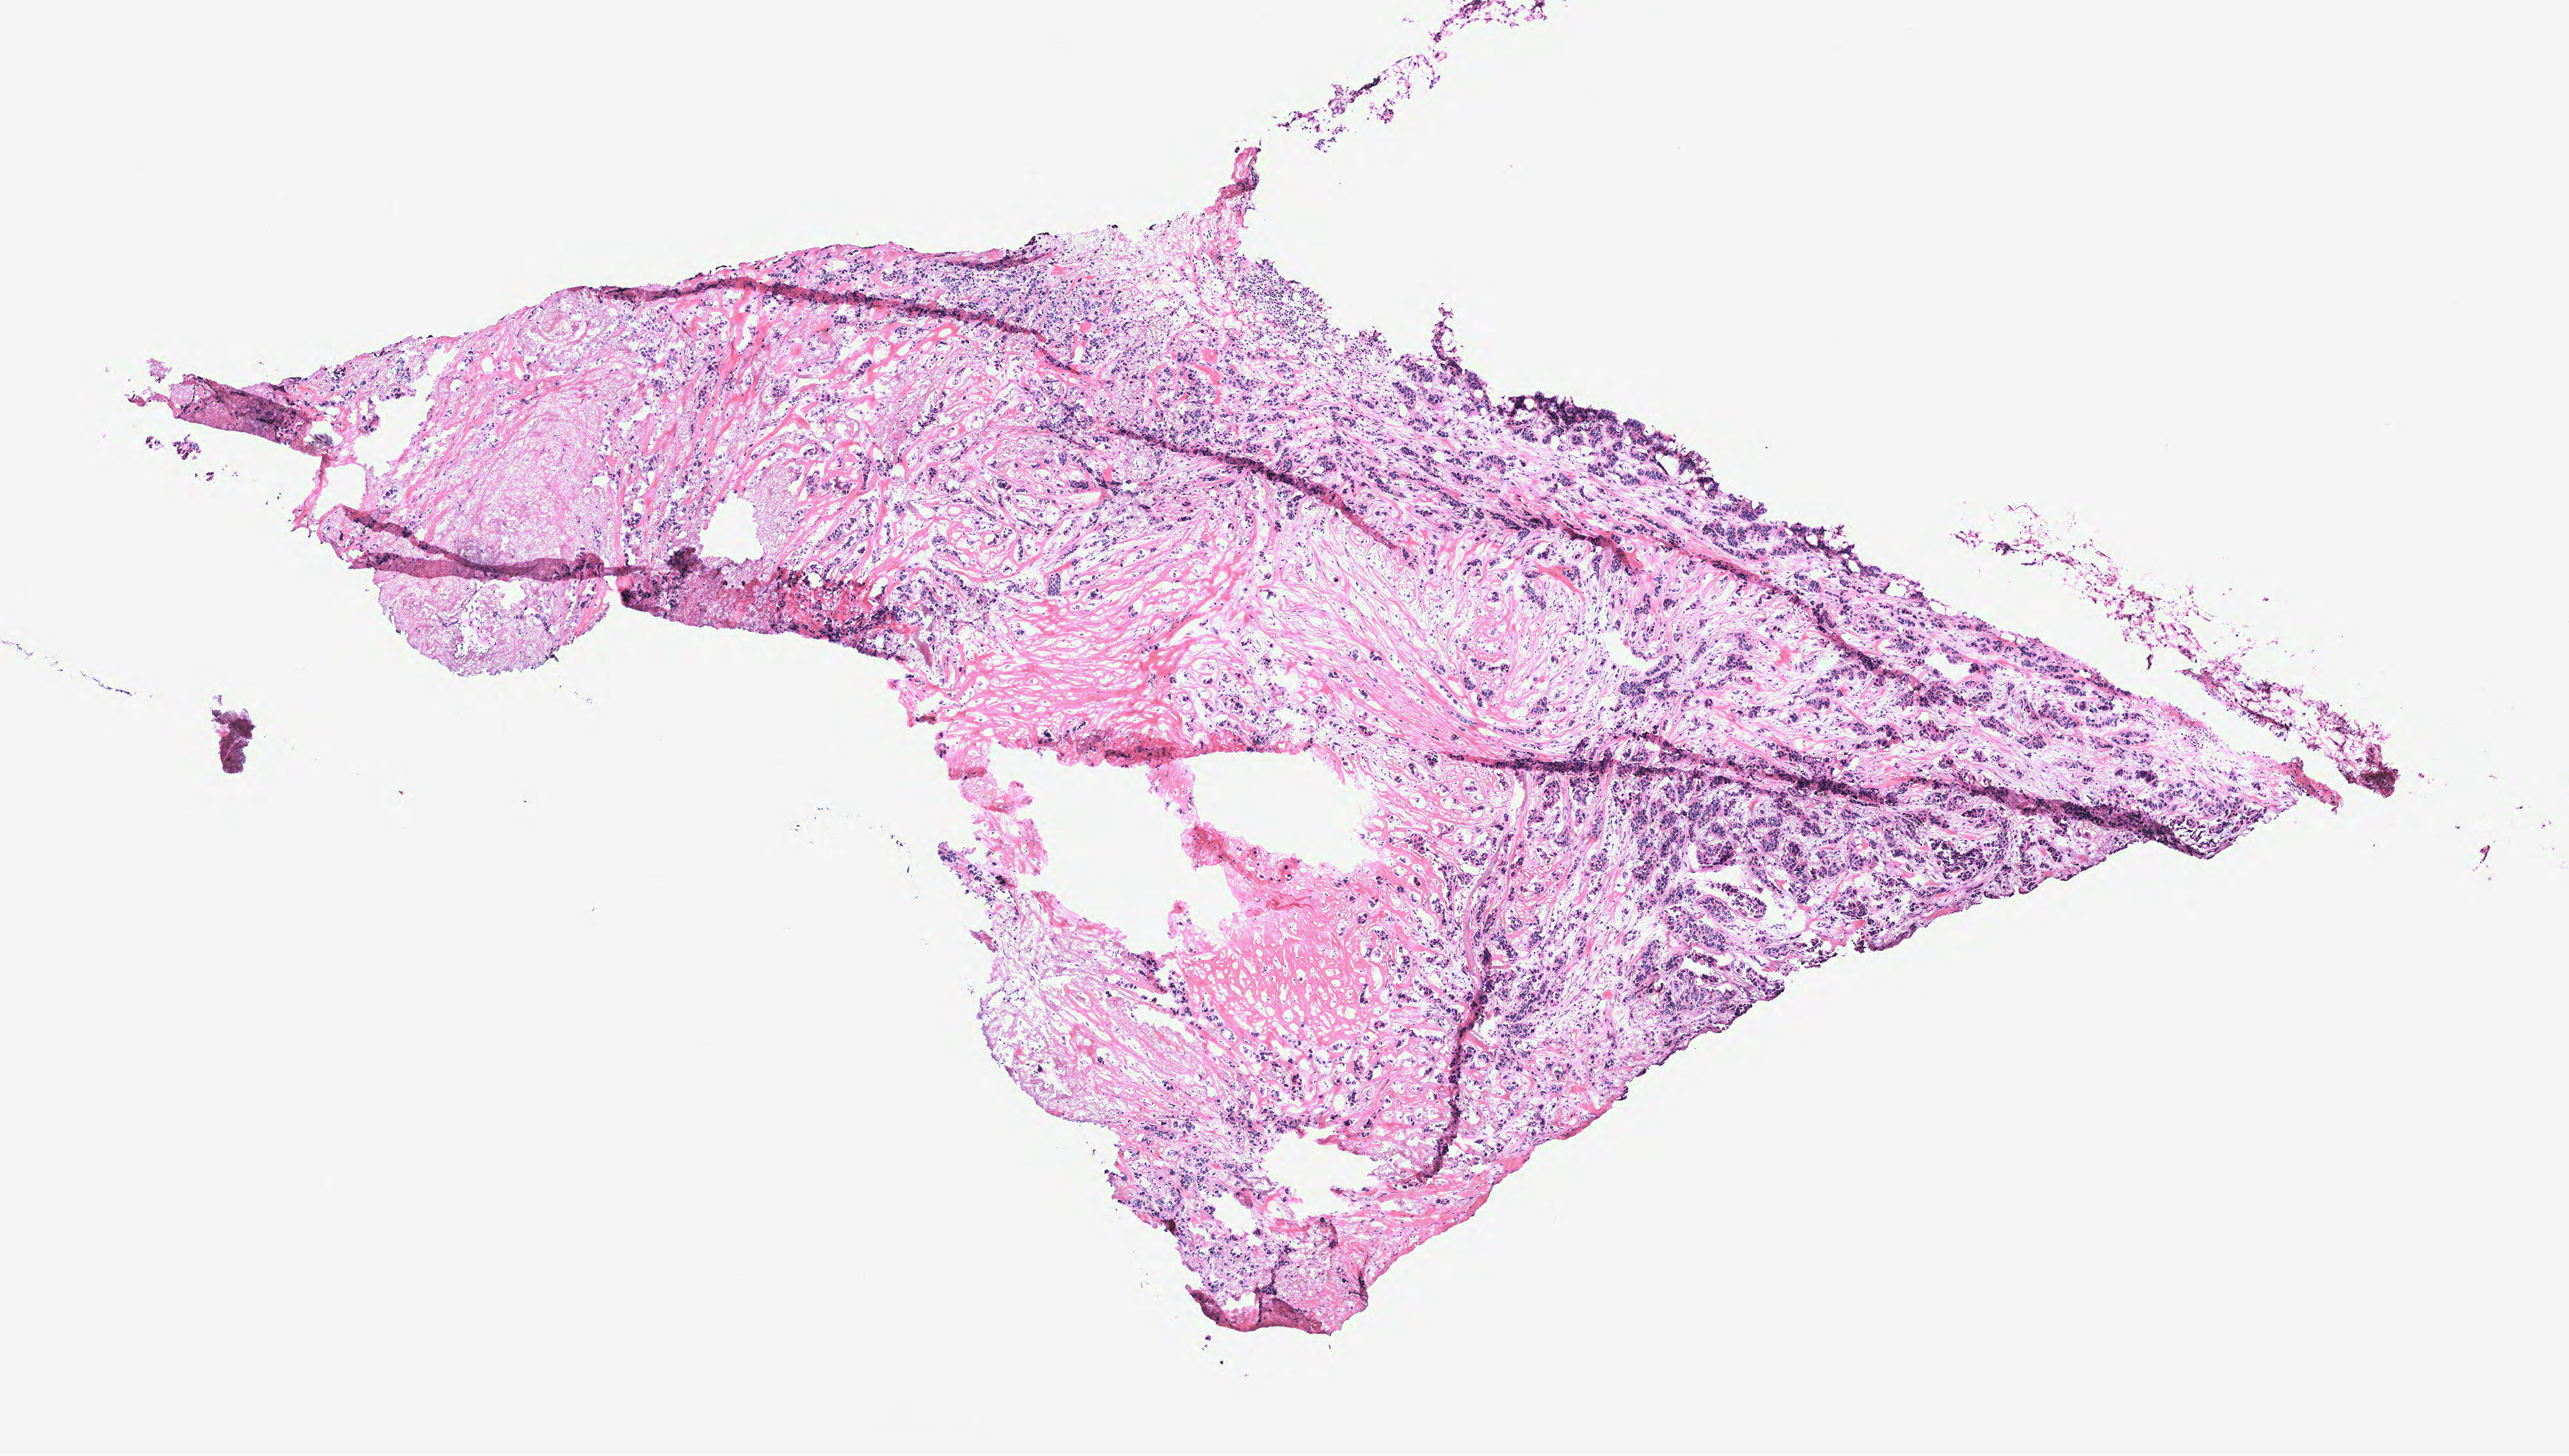
H&E whole-slide image, shown as a low-resolution overview of the whole scanned area (about 7.9 x 4.5 mm). Breast, tissue type not recorded.
Patient diagnosis (cohort enrolment): breast cancer (breast).